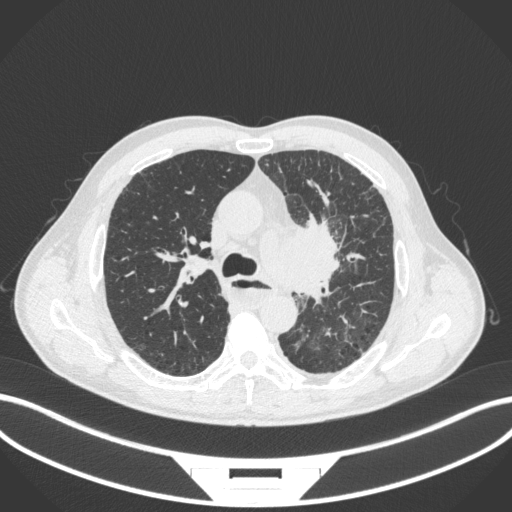
Chest CT, one axial slice. Position 255 of 411 along the scan axis. Lung window (W 1500 / L -600 HU). 1 mm slice thickness. 512 × 512 image matrix, field of view 400 × 400 mm. Male patient, age 57 years. From the clinical record (not read from this slice): clinical TNM (as recorded): T2a N1 M0.
Outlined on this slice (rectangle marked by the reading radiologist):
- lung tumour (recorded histology: squamous cell carcinoma): bounding box <262,216,350,301> (left, top, right, bottom; pixels)